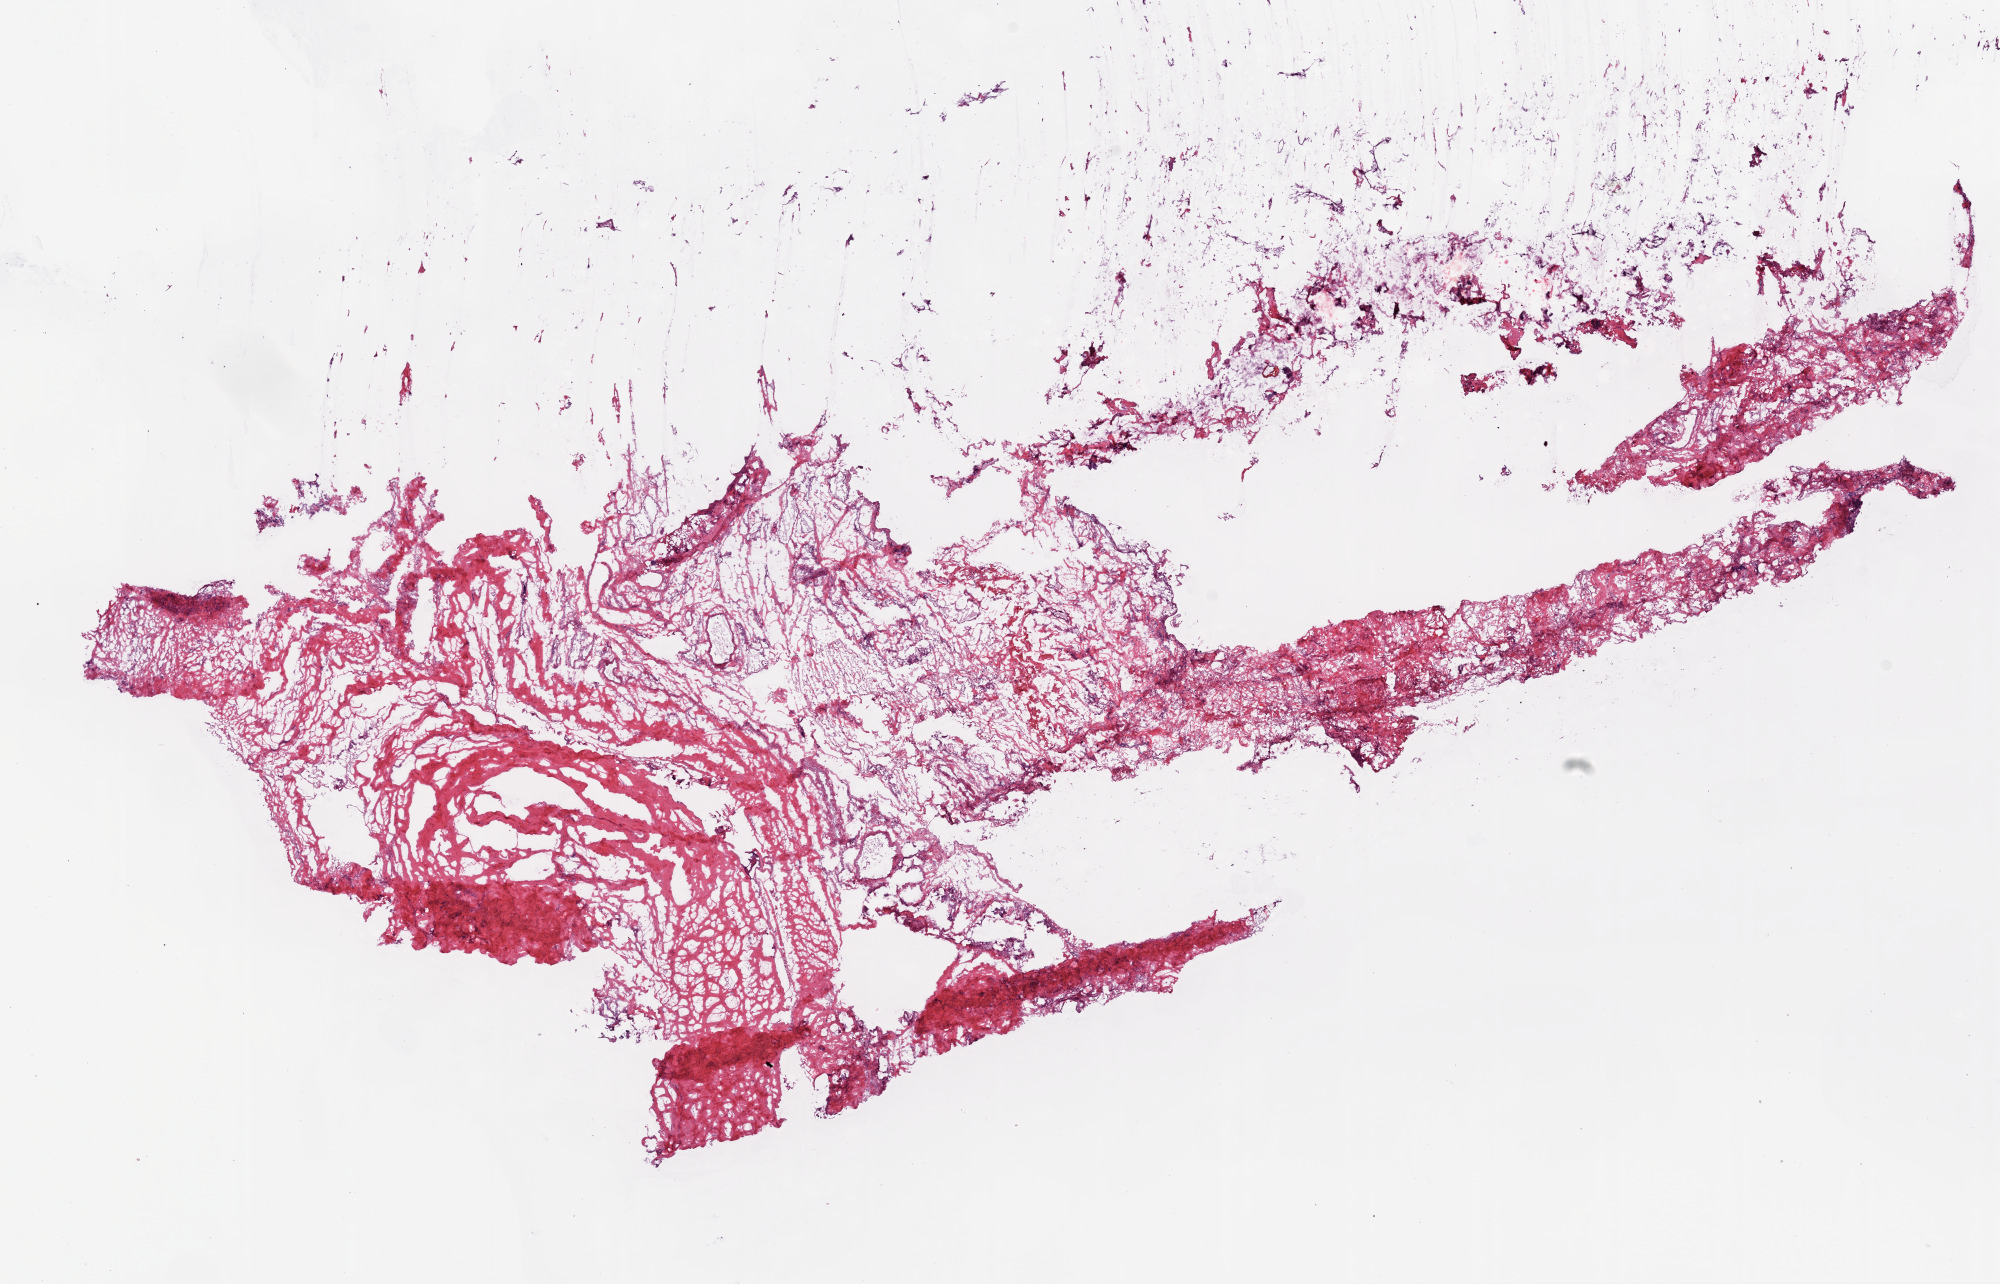
H&E-stained whole-slide image — low-resolution overview of the scanned area, about 16.0 x 10.3 mm, frozen section from the top of the tissue portion, ovary, solid tissue normal (non-tumour tissue) sample. Patient: female, age at initial diagnosis 55 years.
This section: solid tissue normal sample (biorepository sample class). Patient diagnosis: Serous cystadenocarcinoma, NOS.